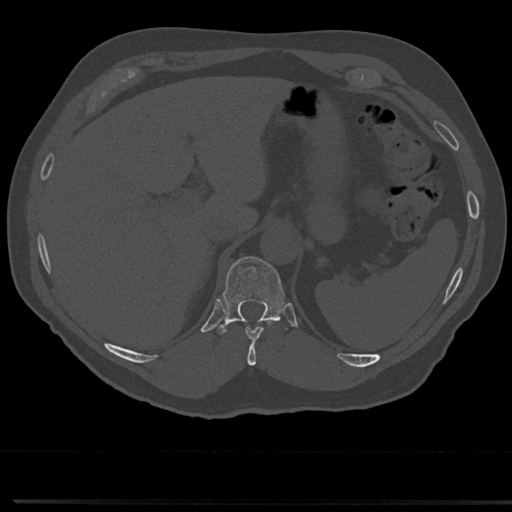
CT including the spine, one axial slice; position 223 of 817 along the scan axis; reconstruction kernel Br40s/3; 120 kVp; bone window (W 1800 / L 400 HU); 512 × 512 image matrix, field of view 355 × 355 mm. Patient: male, 61 years. Case-level facts recorded for this patient, not image findings: primary cancer: prostate.
Annotated regions visible in this slice (semi-automatically segmented with operator editing):
- T10 vertebra: box from (x=233, y=319) to (x=278, y=365) px
- T11 vertebra: (x=223, y=256)–(x=284, y=321)